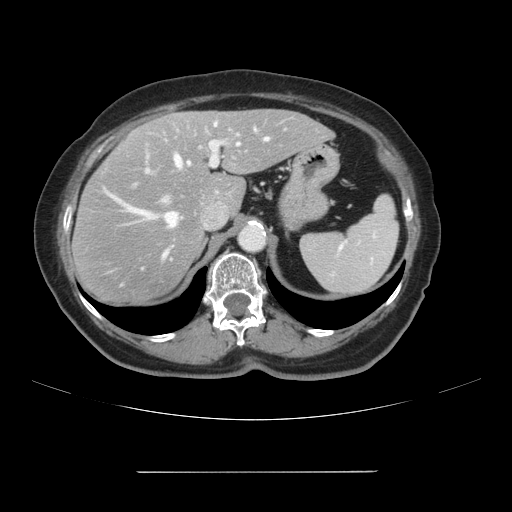
Contrast-enhanced abdominal CT, one axial slice. Slice 71 of 111 in the series (ordered by position). Intravenous contrast given. Soft-tissue window (W 400 / L 40 HU). 512 × 512 image matrix, field of view 400 × 400 mm. Female patient, age 74 years. Case-level facts recorded for this patient, not image findings: diagnosis: colorectal cancer liver metastases, imaged before liver resection; multiple liver metastases: yes; largest metastasis: 1.1 cm; disease in both lobes: yes.
Outlined on this slice (outlined manually by an expert reader):
- hepatic veins: bounding box <106,129,269,286> (left, top, right, bottom; pixels)
- liver: <74,110,331,305>
- planned liver remnant (the part of the liver to remain after resection): <152,110,331,213>
- portal vein (with intrahepatic branches): <146,123,222,202>